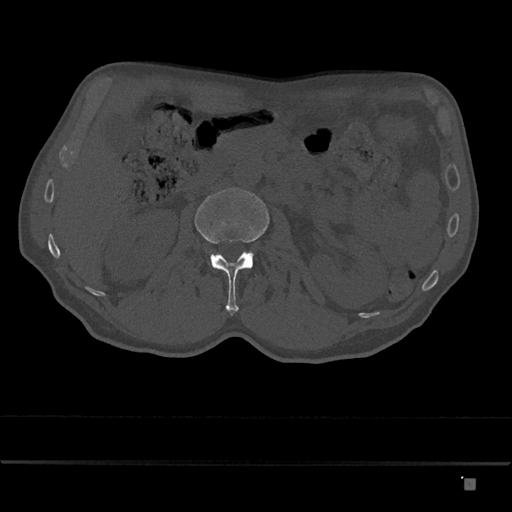
CT including the spine, one axial slice. Position 468 of 797 along the scan axis. Reconstruction kernel Br40s/3. 120 kVp. Bone window (W 1800 / L 400 HU). 512 × 512 image matrix, field of view 390 × 390 mm. Patient: male, 72 years. Case-level facts recorded for this patient, not image findings: primary cancer: prostate.
Outlined on this slice (semi-automatic segmentation, software-assisted and operator-edited):
- L2 vertebra: bounding box (x1, y1, x2, y2) in pixels: (194, 188, 270, 315)